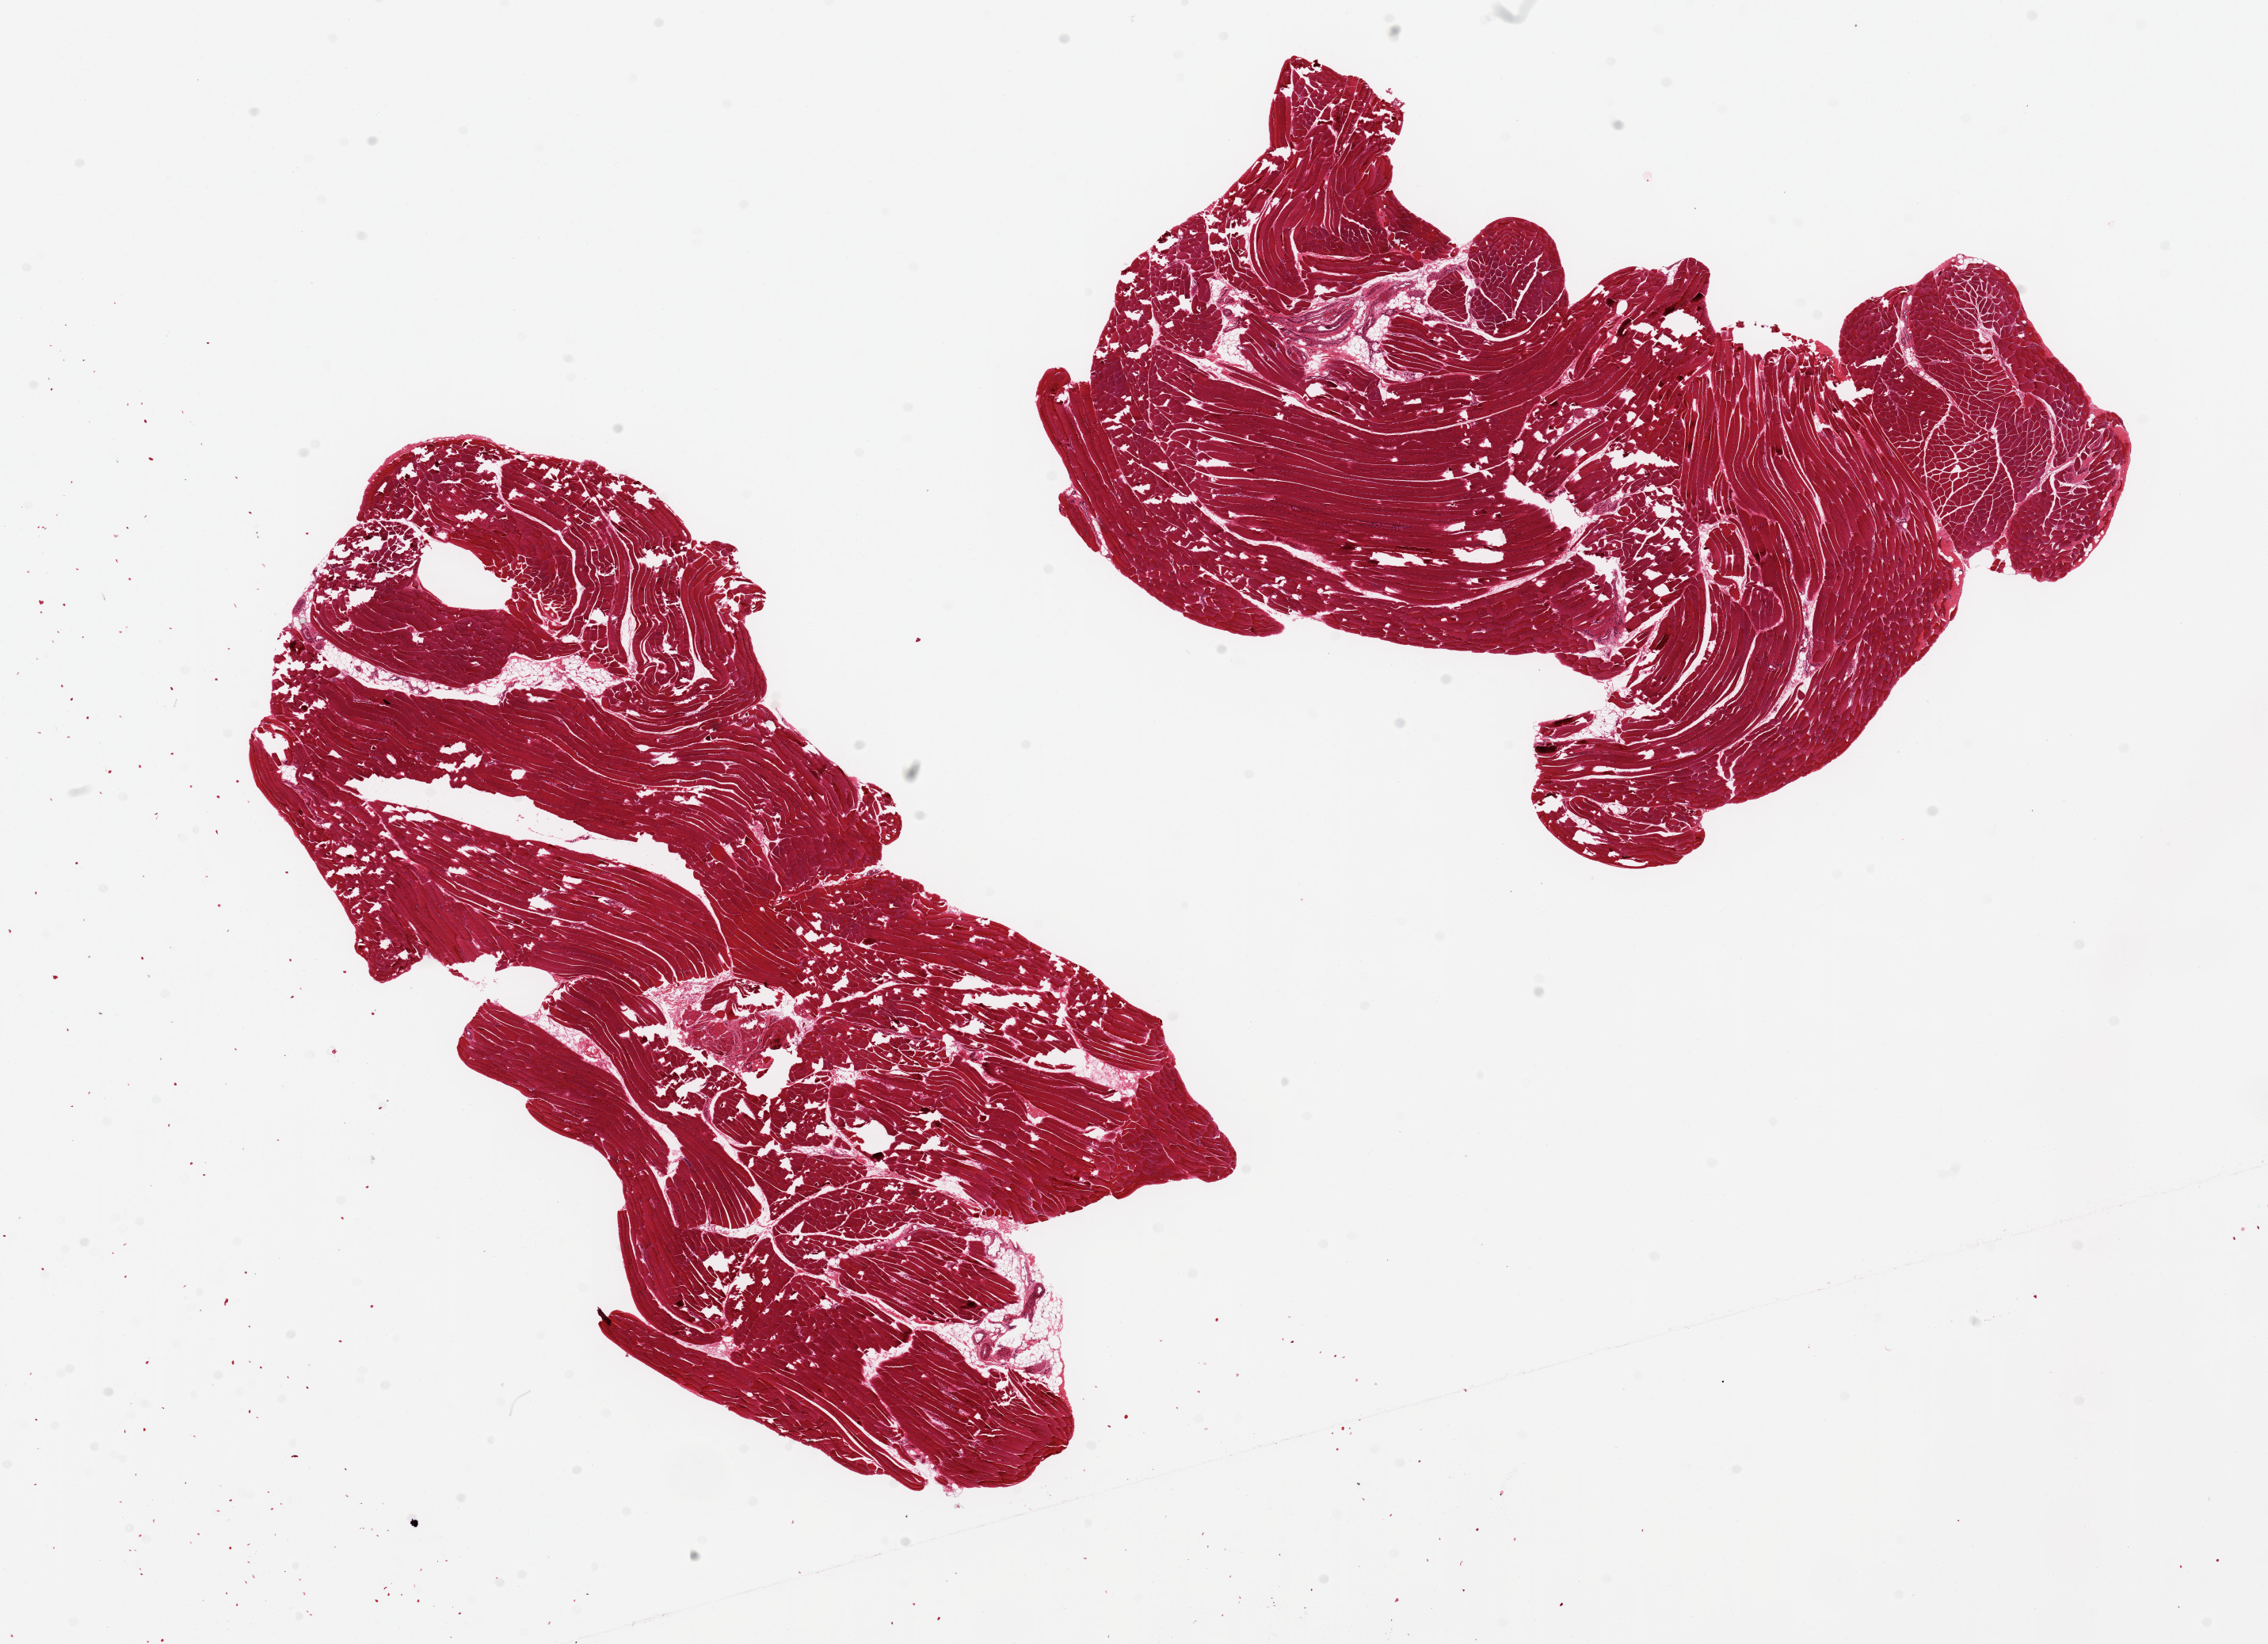
Digitized hematoxylin and eosin (H&E)-stained section — shown as a low-resolution overview of the whole scanned area (about 22.6 x 16.4 mm); PAXgene-fixed paraffin-embedded (PFPE) section; section of skeletal muscle (target tissue); donor tissue sample. Male donor.
Review note (as recorded): 2 ~ 9x4.5mm pieces. Areas of underfixation, tears/holes. ~ 10% interspersed fat.